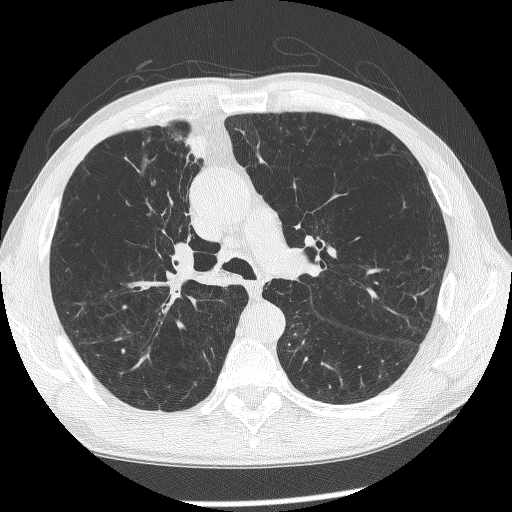
Axial slice from a low-dose chest CT screening exam; baseline screening round; lung window (W 1500 / L -600 HU); 1.25 mm slice thickness; lung (sharp) reconstruction kernel (BONE); 512 × 512 image matrix. Male participant, aged 60 years at enrolment. Current smoker at enrolment.
Expert-annotated lung lesion, bounding box [x1, y1, x2, y2] px = [144, 210, 226, 302]. Reader record for this screening exam (exam-level; its link to the box is not recorded): non-calcified nodule or mass ≥4 mm, right upper lobe, 12 × 8 mm, spiculated (stellate) margins, mixed attenuation. Official screen result: positive, change unspecified: nodule(s) >= 4 mm or enlarging nodule(s), mass(es), or other non-specific abnormalities suspicious for lung cancer. Later outcome: lung cancer diagnosed 208 days after this screen — squamous cell carcinoma, NOS, right upper lobe, right middle lobe, right main stem bronchus, poorly differentiated (G3), stage IV (AJCC 6th edition).